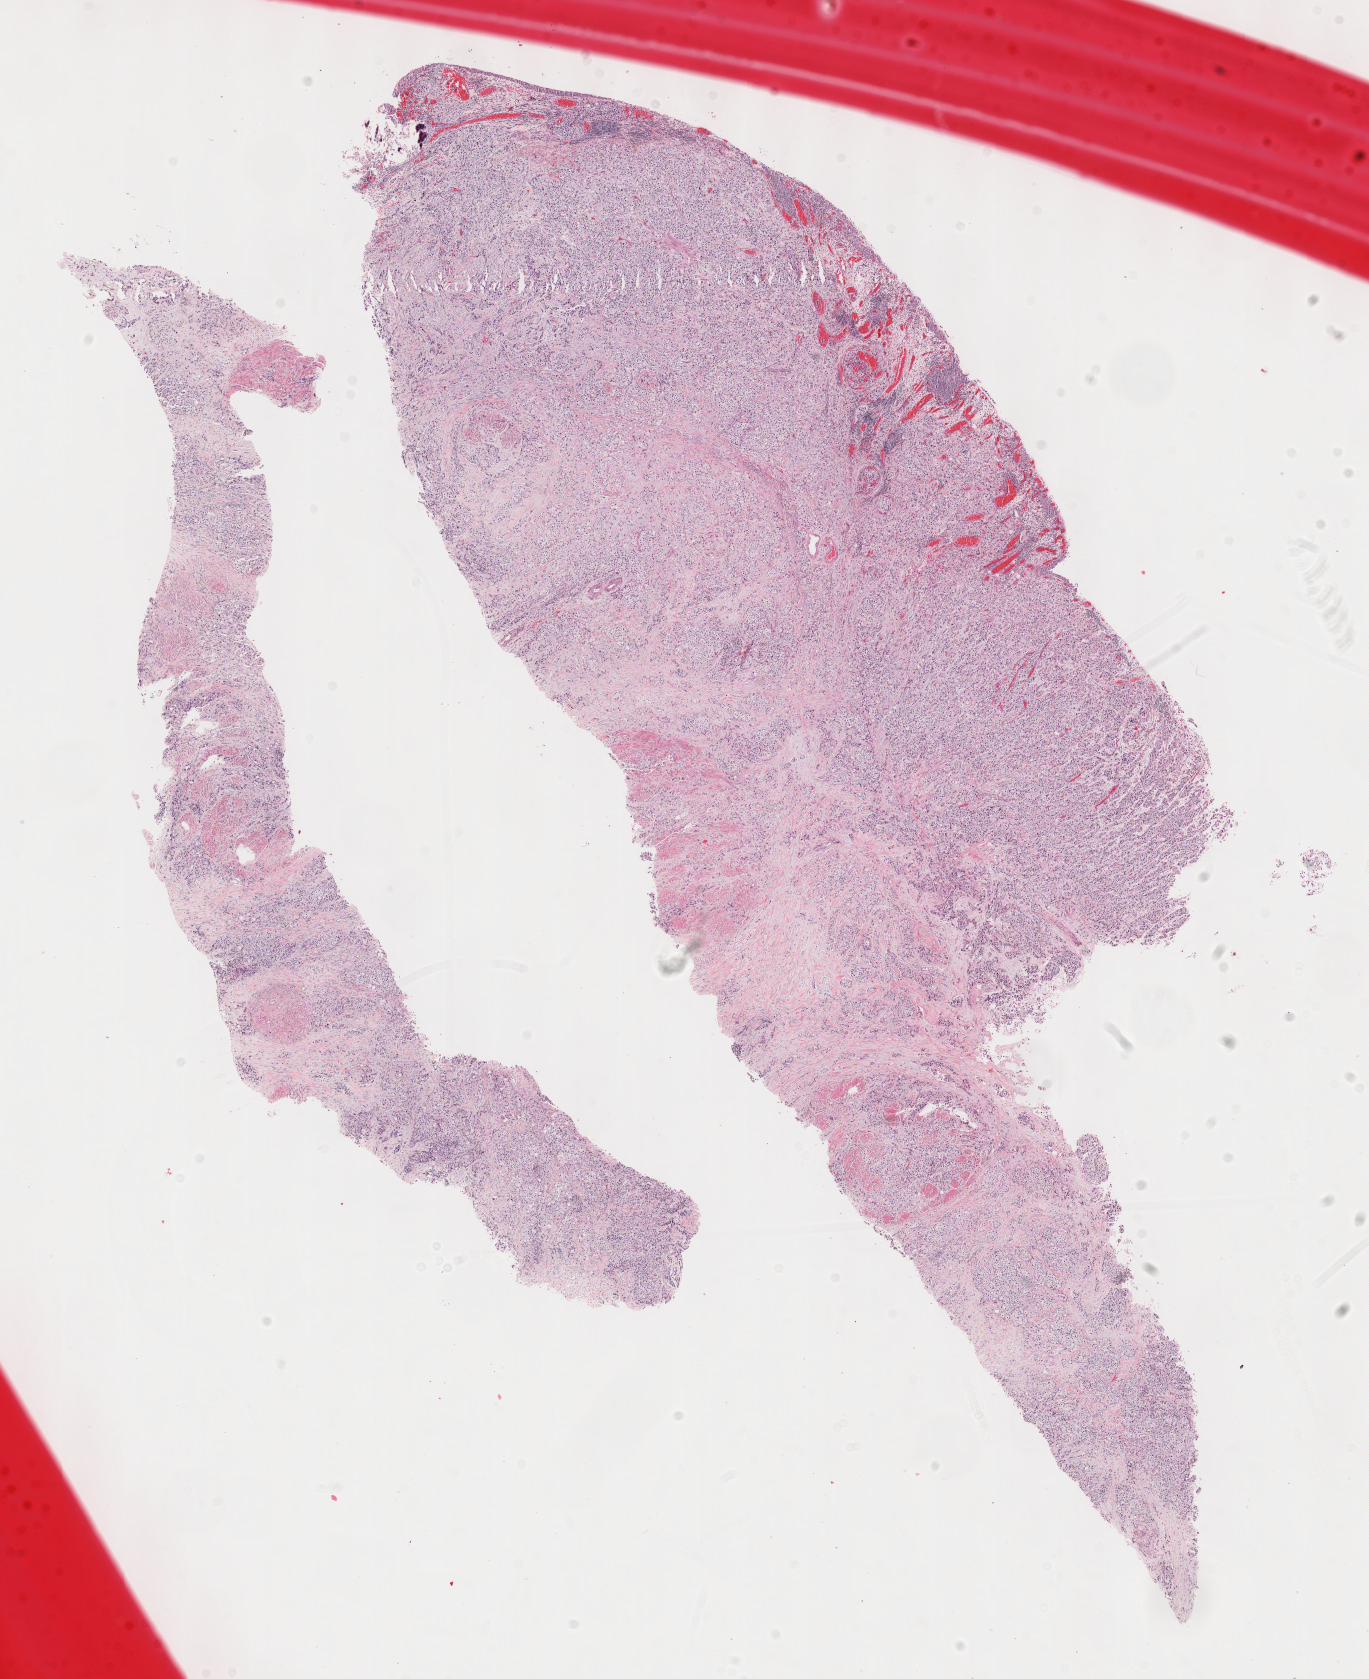
Hematoxylin and eosin (H&E) stained whole-slide image, shown as a low-resolution overview of the whole scanned area (about 11.1 x 13.6 mm). Formalin-fixed paraffin-embedded (FFPE) diagnostic section. Bladder, primary tumour sample. Female, age 60 years at initial diagnosis. Histologic grade: high grade.
- lymph nodes positive (case pathology): 20 of 48 examined
- AJCC pathologic stage: IV
- pathologic diagnosis: Transitional cell carcinoma